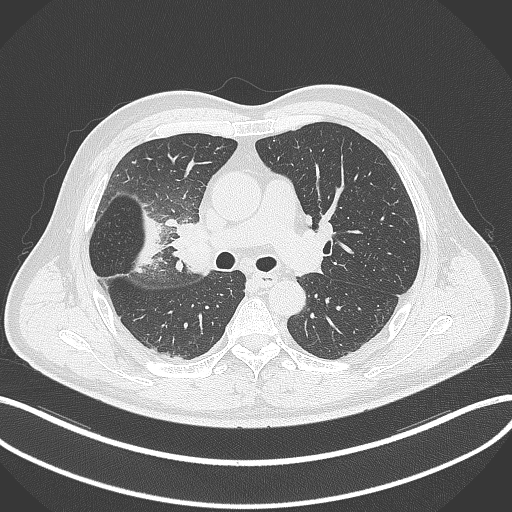
Chest CT, one axial slice; position 199 of 348 along the scan axis; reconstruction kernel B70f; lung window (W 1500 / L -600 HU); 1 mm slice thickness; 512 × 512 image matrix, field of view 400 × 400 mm. Male patient, age 55 years. Case-level facts recorded for this patient, not image findings: clinical TNM (as recorded): T3 N2 M1.
Outlined on this slice (rectangle marked by the reading radiologist):
- lung tumour (recorded histology: adenocarcinoma): box from (x=133, y=205) to (x=167, y=279) px